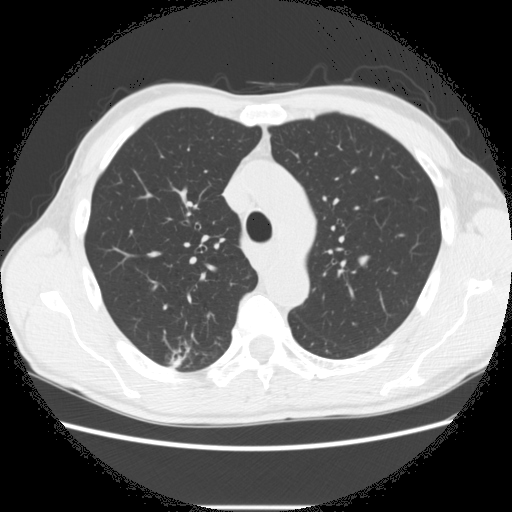
Low-dose screening chest CT, one axial slice; position 203 of 282 along the scan axis; lung window (W 1500 / L -600 HU); 2.5 mm slice thickness; 512 × 512 image matrix, field of view 360 × 360 mm.
Annotated regions visible in this slice (manually delineated by an expert):
- lesion 1 (tumor, upper lobe of right lung): bounding box (x1, y1, x2, y2) in pixels: (170, 354, 184, 369)